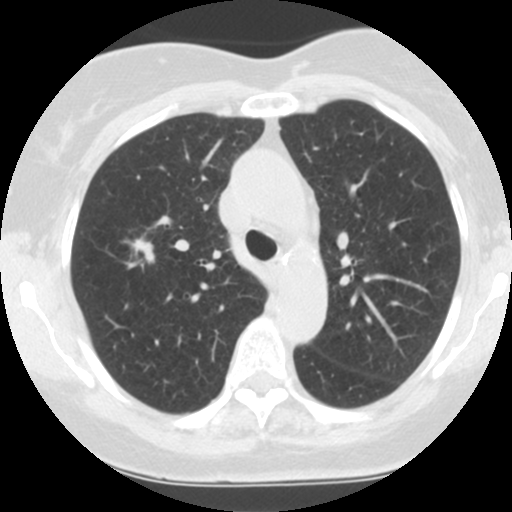
Low-dose screening chest CT, one axial slice. Position 75 of 106 along the scan axis. 120 kVp. One of 2 acquisitions stored at this slice position. Lung window (W 1500 / L -600 HU). 2.5 mm slice thickness. 512 × 512 image matrix, field of view 280 × 280 mm.
Structures marked on this image (manually delineated by an expert):
- lesion 1 (tumor, upper lobe of right lung): box from (x=134, y=240) to (x=153, y=260) px